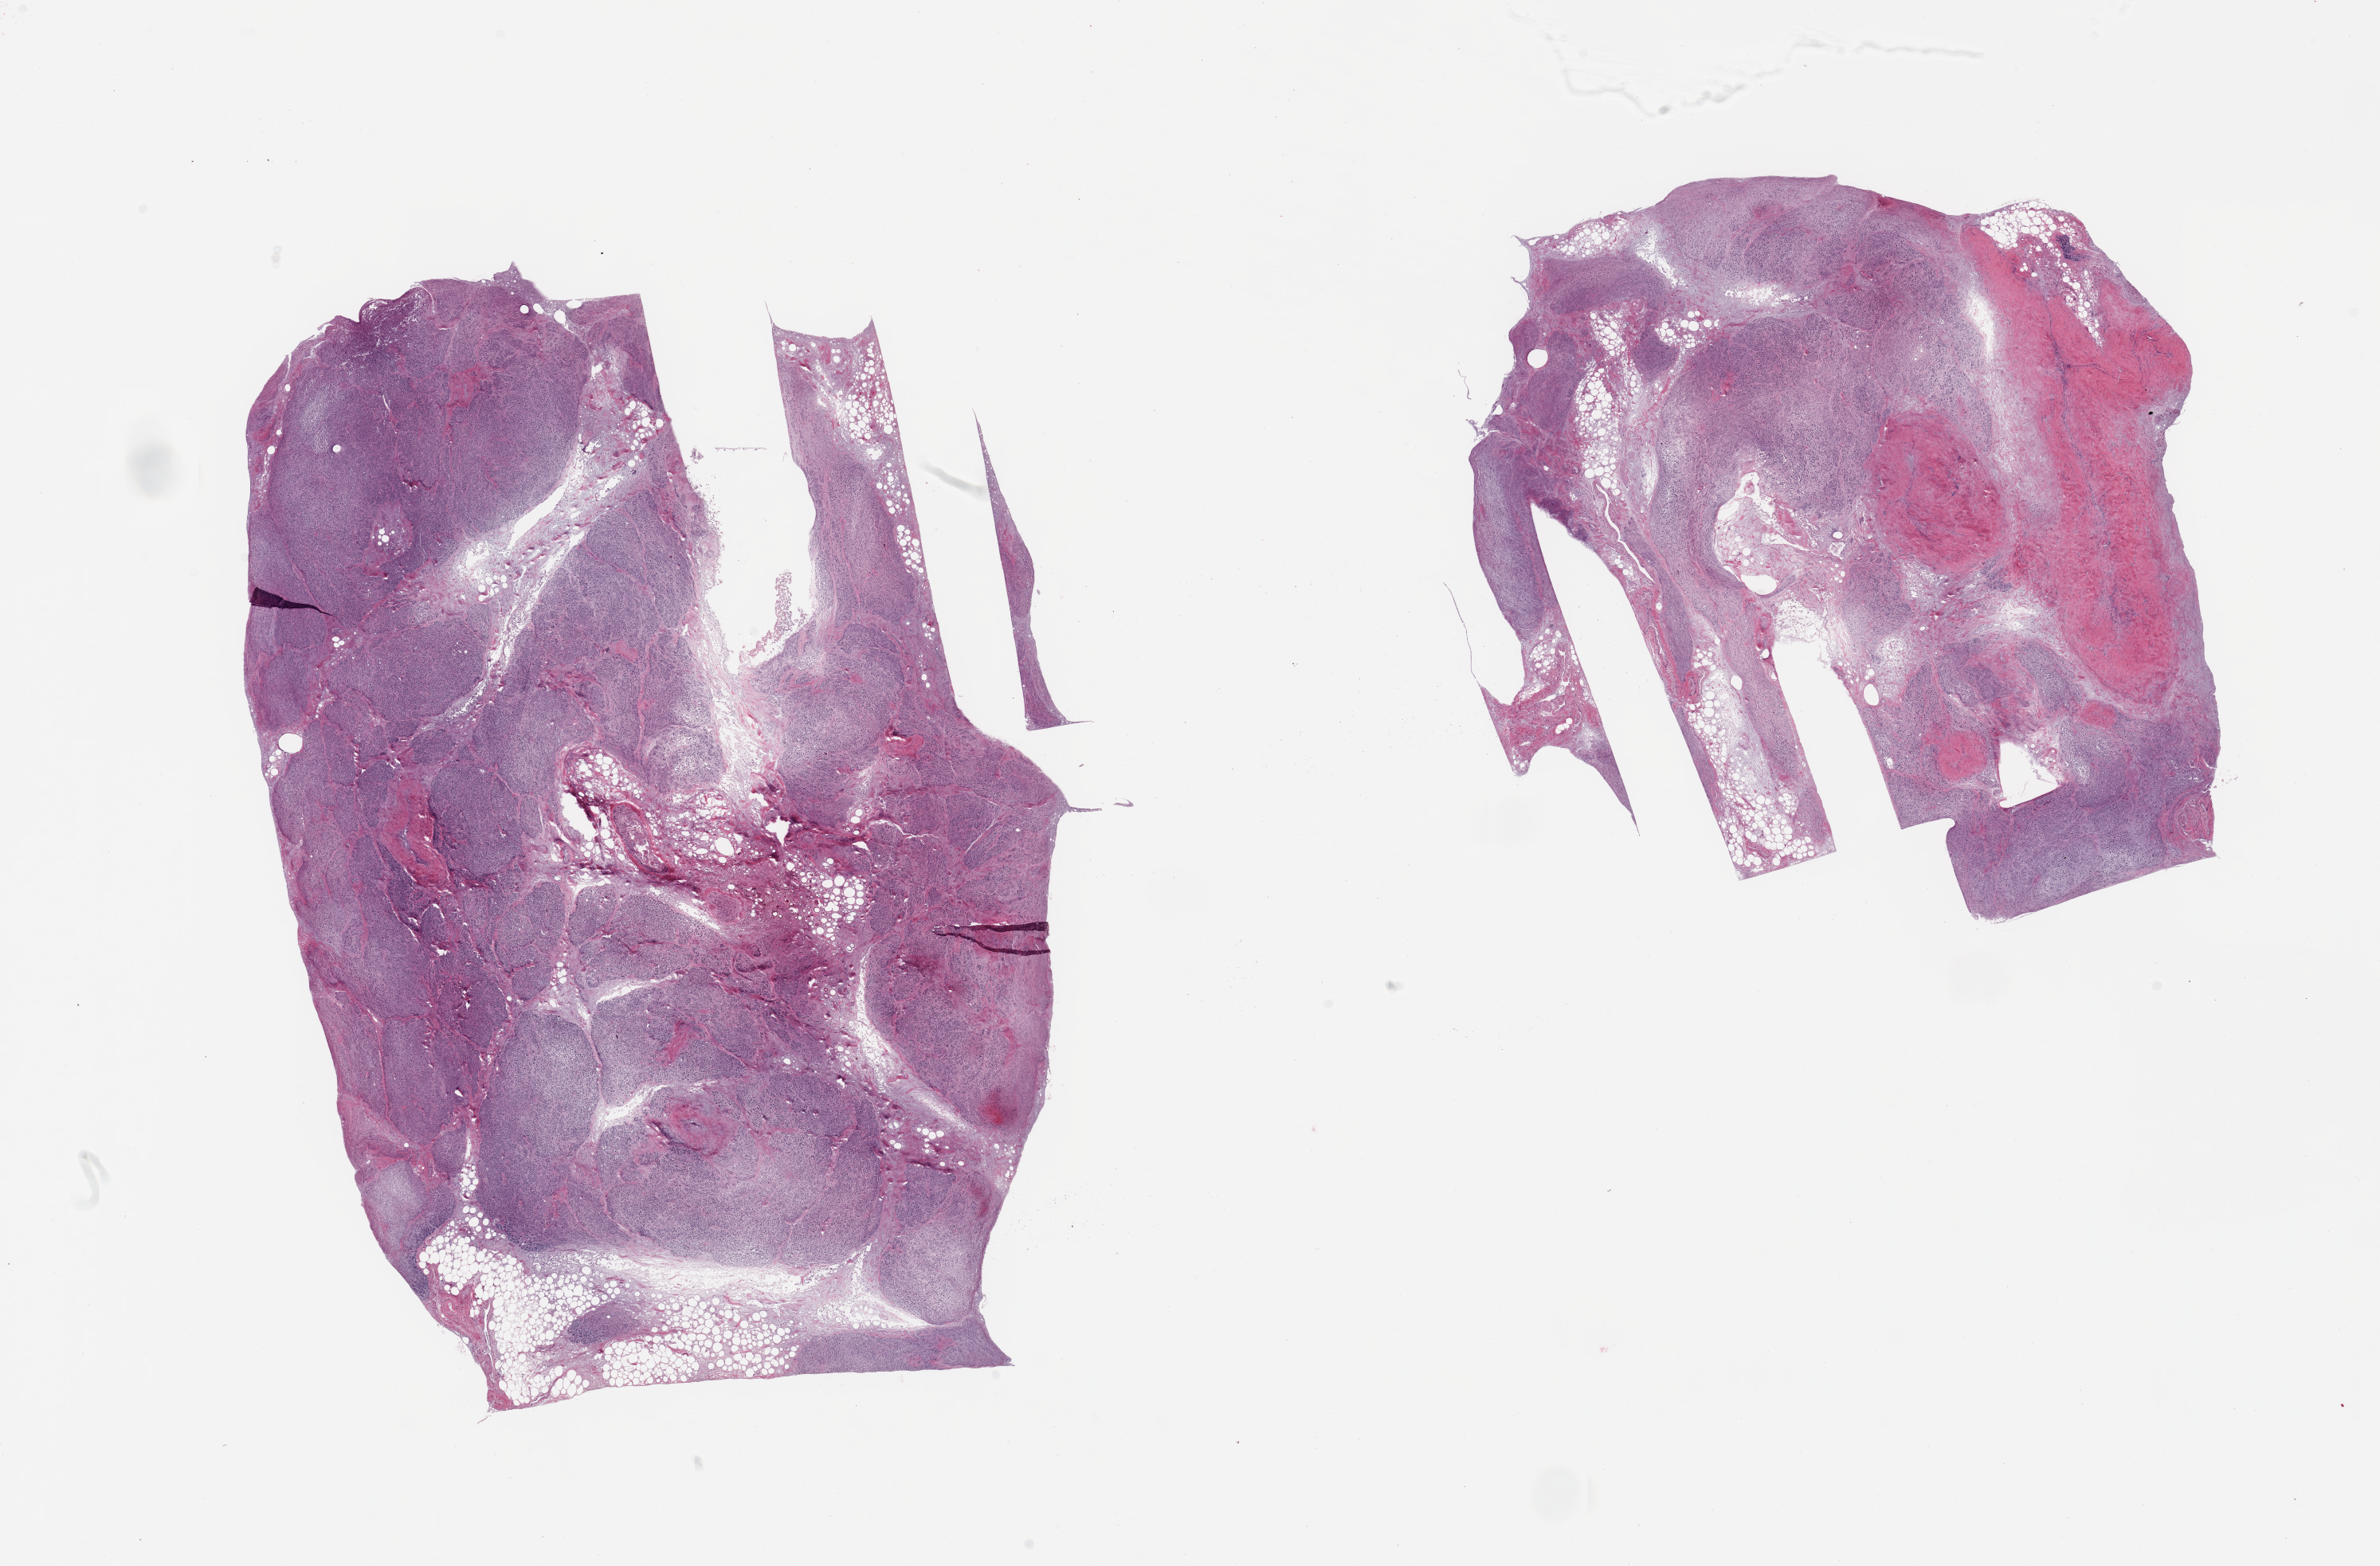
Digitized hematoxylin and eosin (H&E)-stained section — shown as a low-resolution overview of the whole scanned area (about 23.6 x 15.6 mm). PAXgene-fixed paraffin-embedded (PFPE) section. Target tissue: pancreas. Donor tissue sample. Donor sex: female.
Reviewer comment on this tissue sample: 2 pieces; marked autolysis.